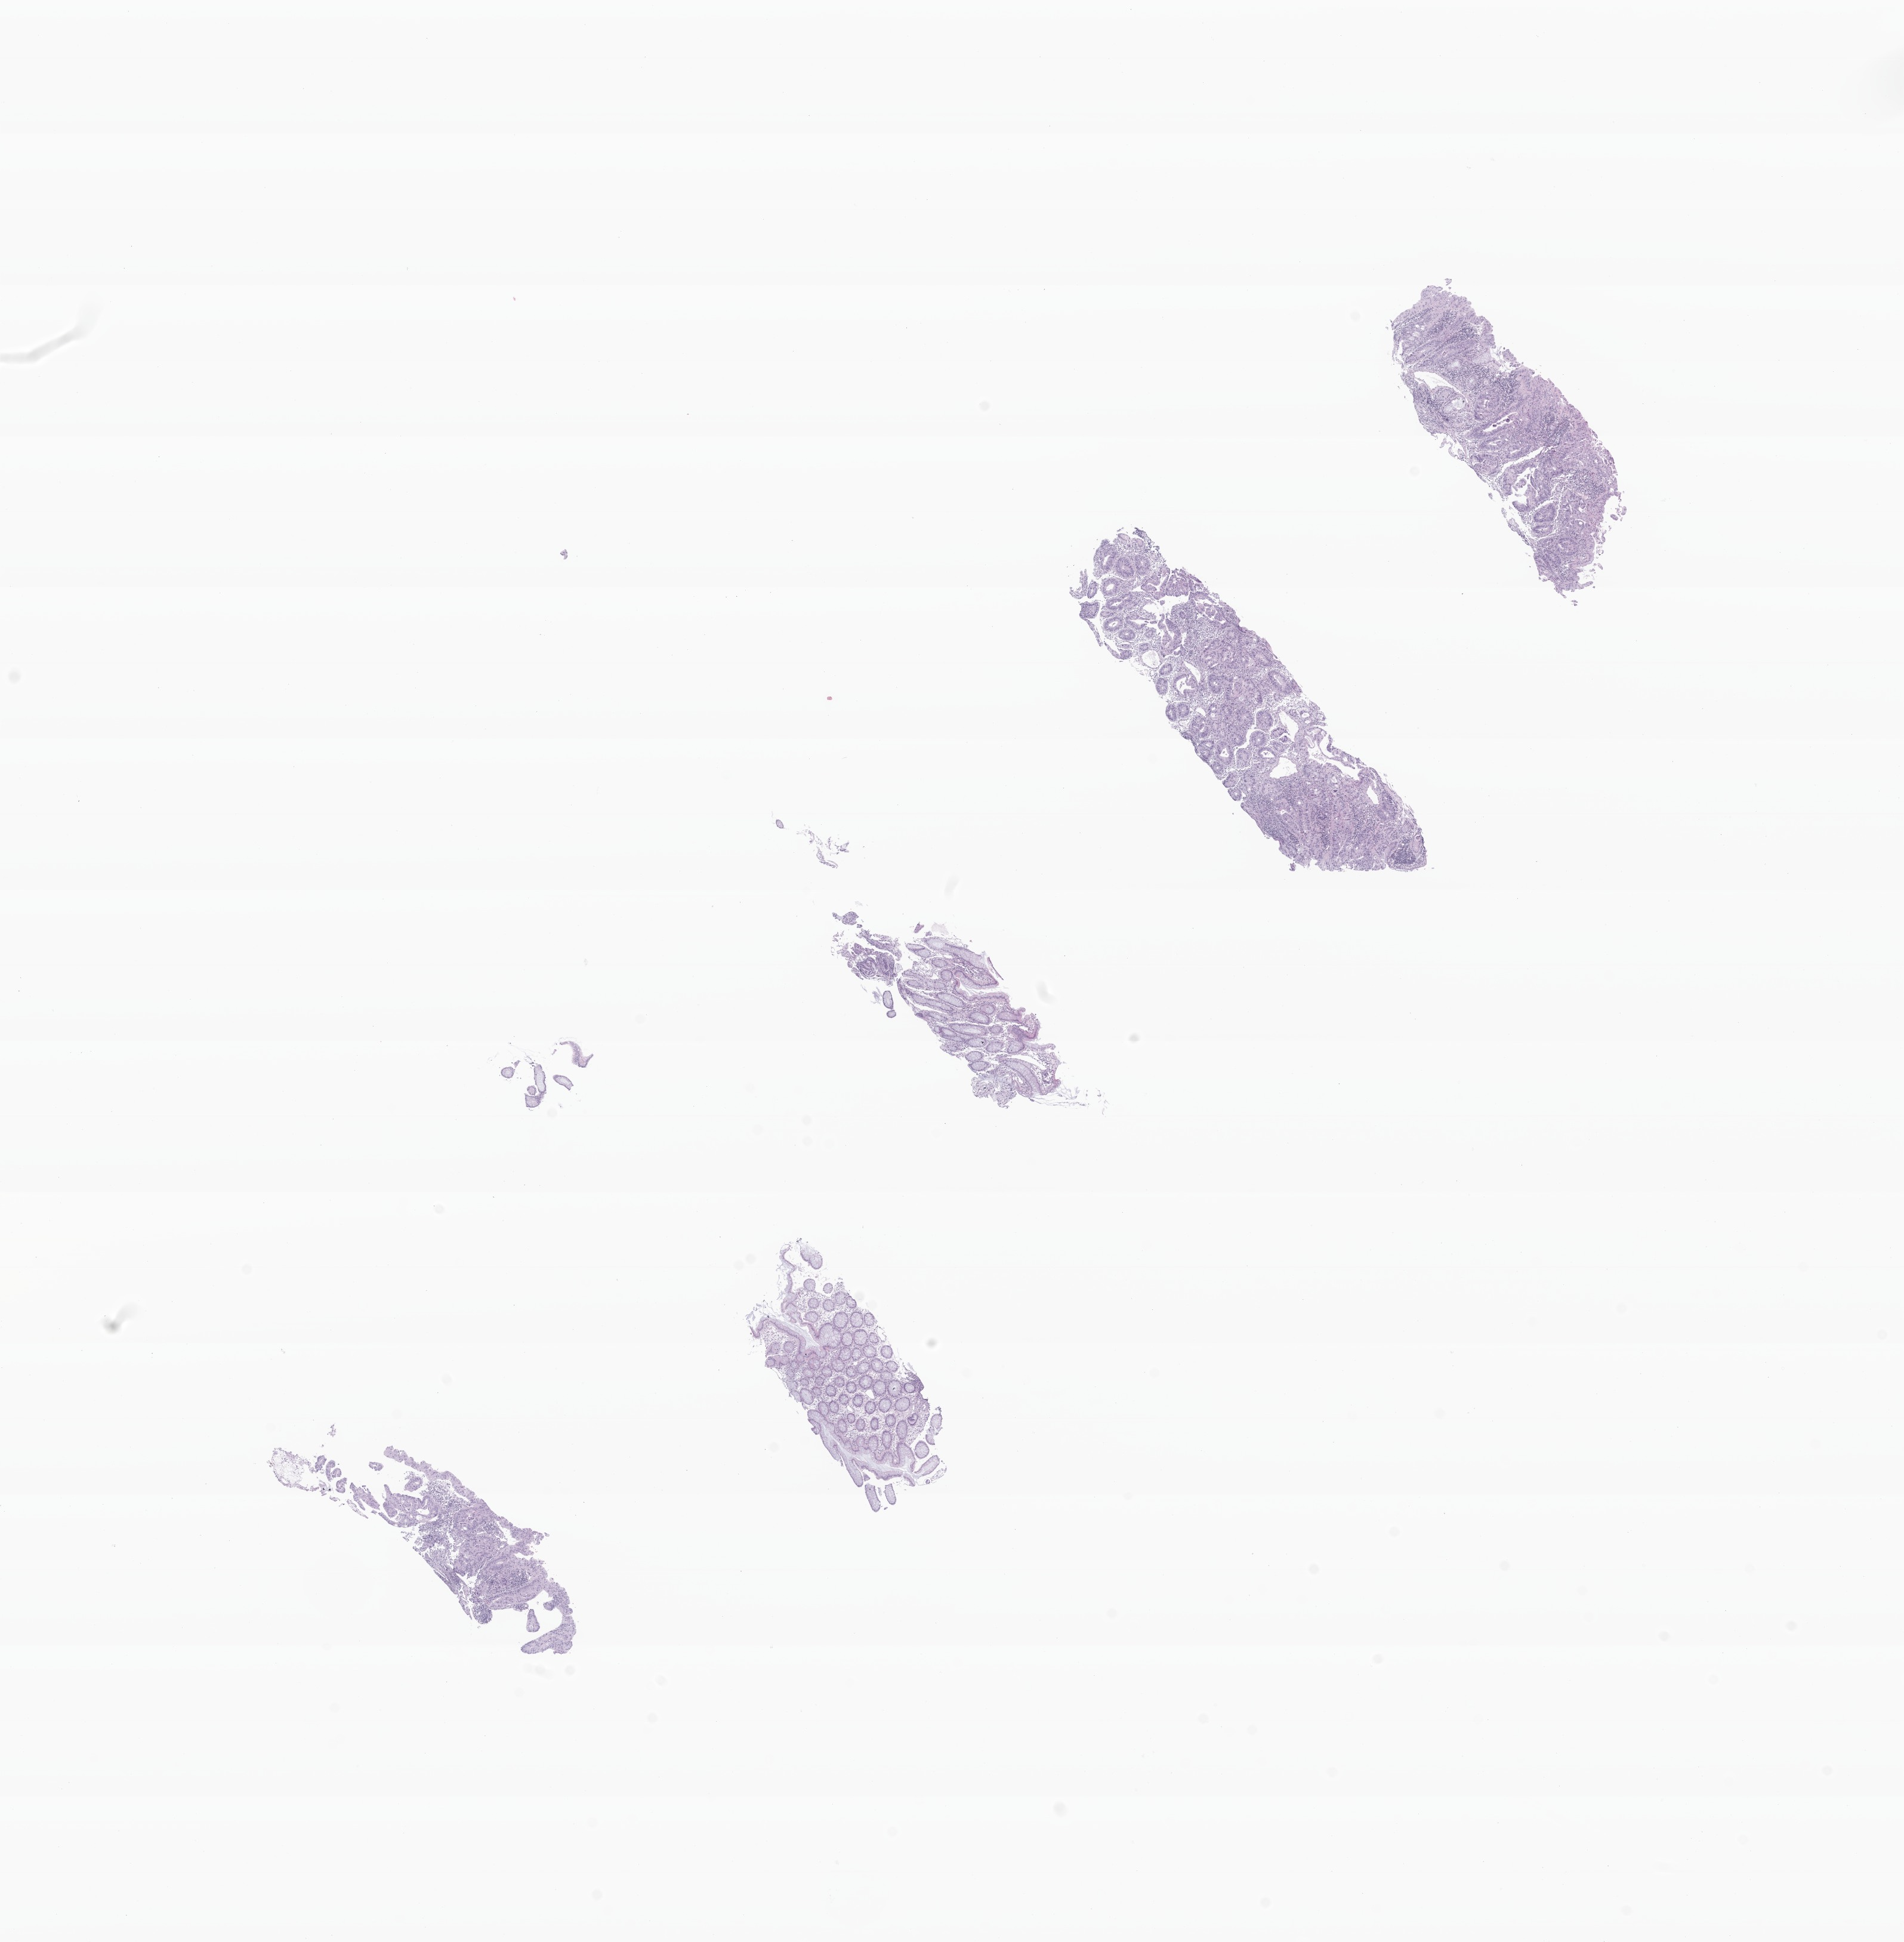
Hematoxylin and eosin (H&E) whole-slide image of tumor tissue from the colon — a low-resolution overview of the entire scanned area, about 13.4 x 13.7 mm. Formalin-fixed, paraffin-embedded (FFPE) tissue. Patient male; age 147 months (12 years 3 months).
* diagnosis (ICD-O-3 morphology term): Adenocarcinoma, NOS